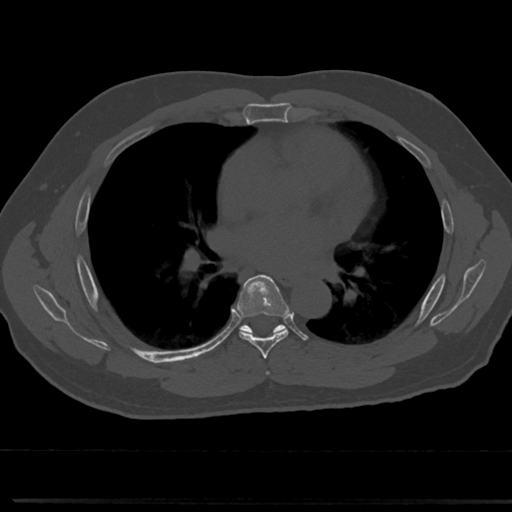
CT including the spine, one axial slice. Slice 439 of 817 in the series (ordered by position). Reconstruction kernel Br40s/3. 120 kVp. Bone window (W 1800 / L 400 HU). 0.5 mm slice thickness. 512 × 512 image matrix, field of view 355 × 355 mm. Patient: male, 61 years. Case-level facts recorded for this patient, not image findings: primary cancer: prostate.
Annotated regions visible in this slice (semi-automatically segmented with operator editing):
- T5 vertebra: bounding box (x1, y1, x2, y2) in pixels: (264, 361, 273, 377)
- T6 vertebra: (230, 277, 308, 351)